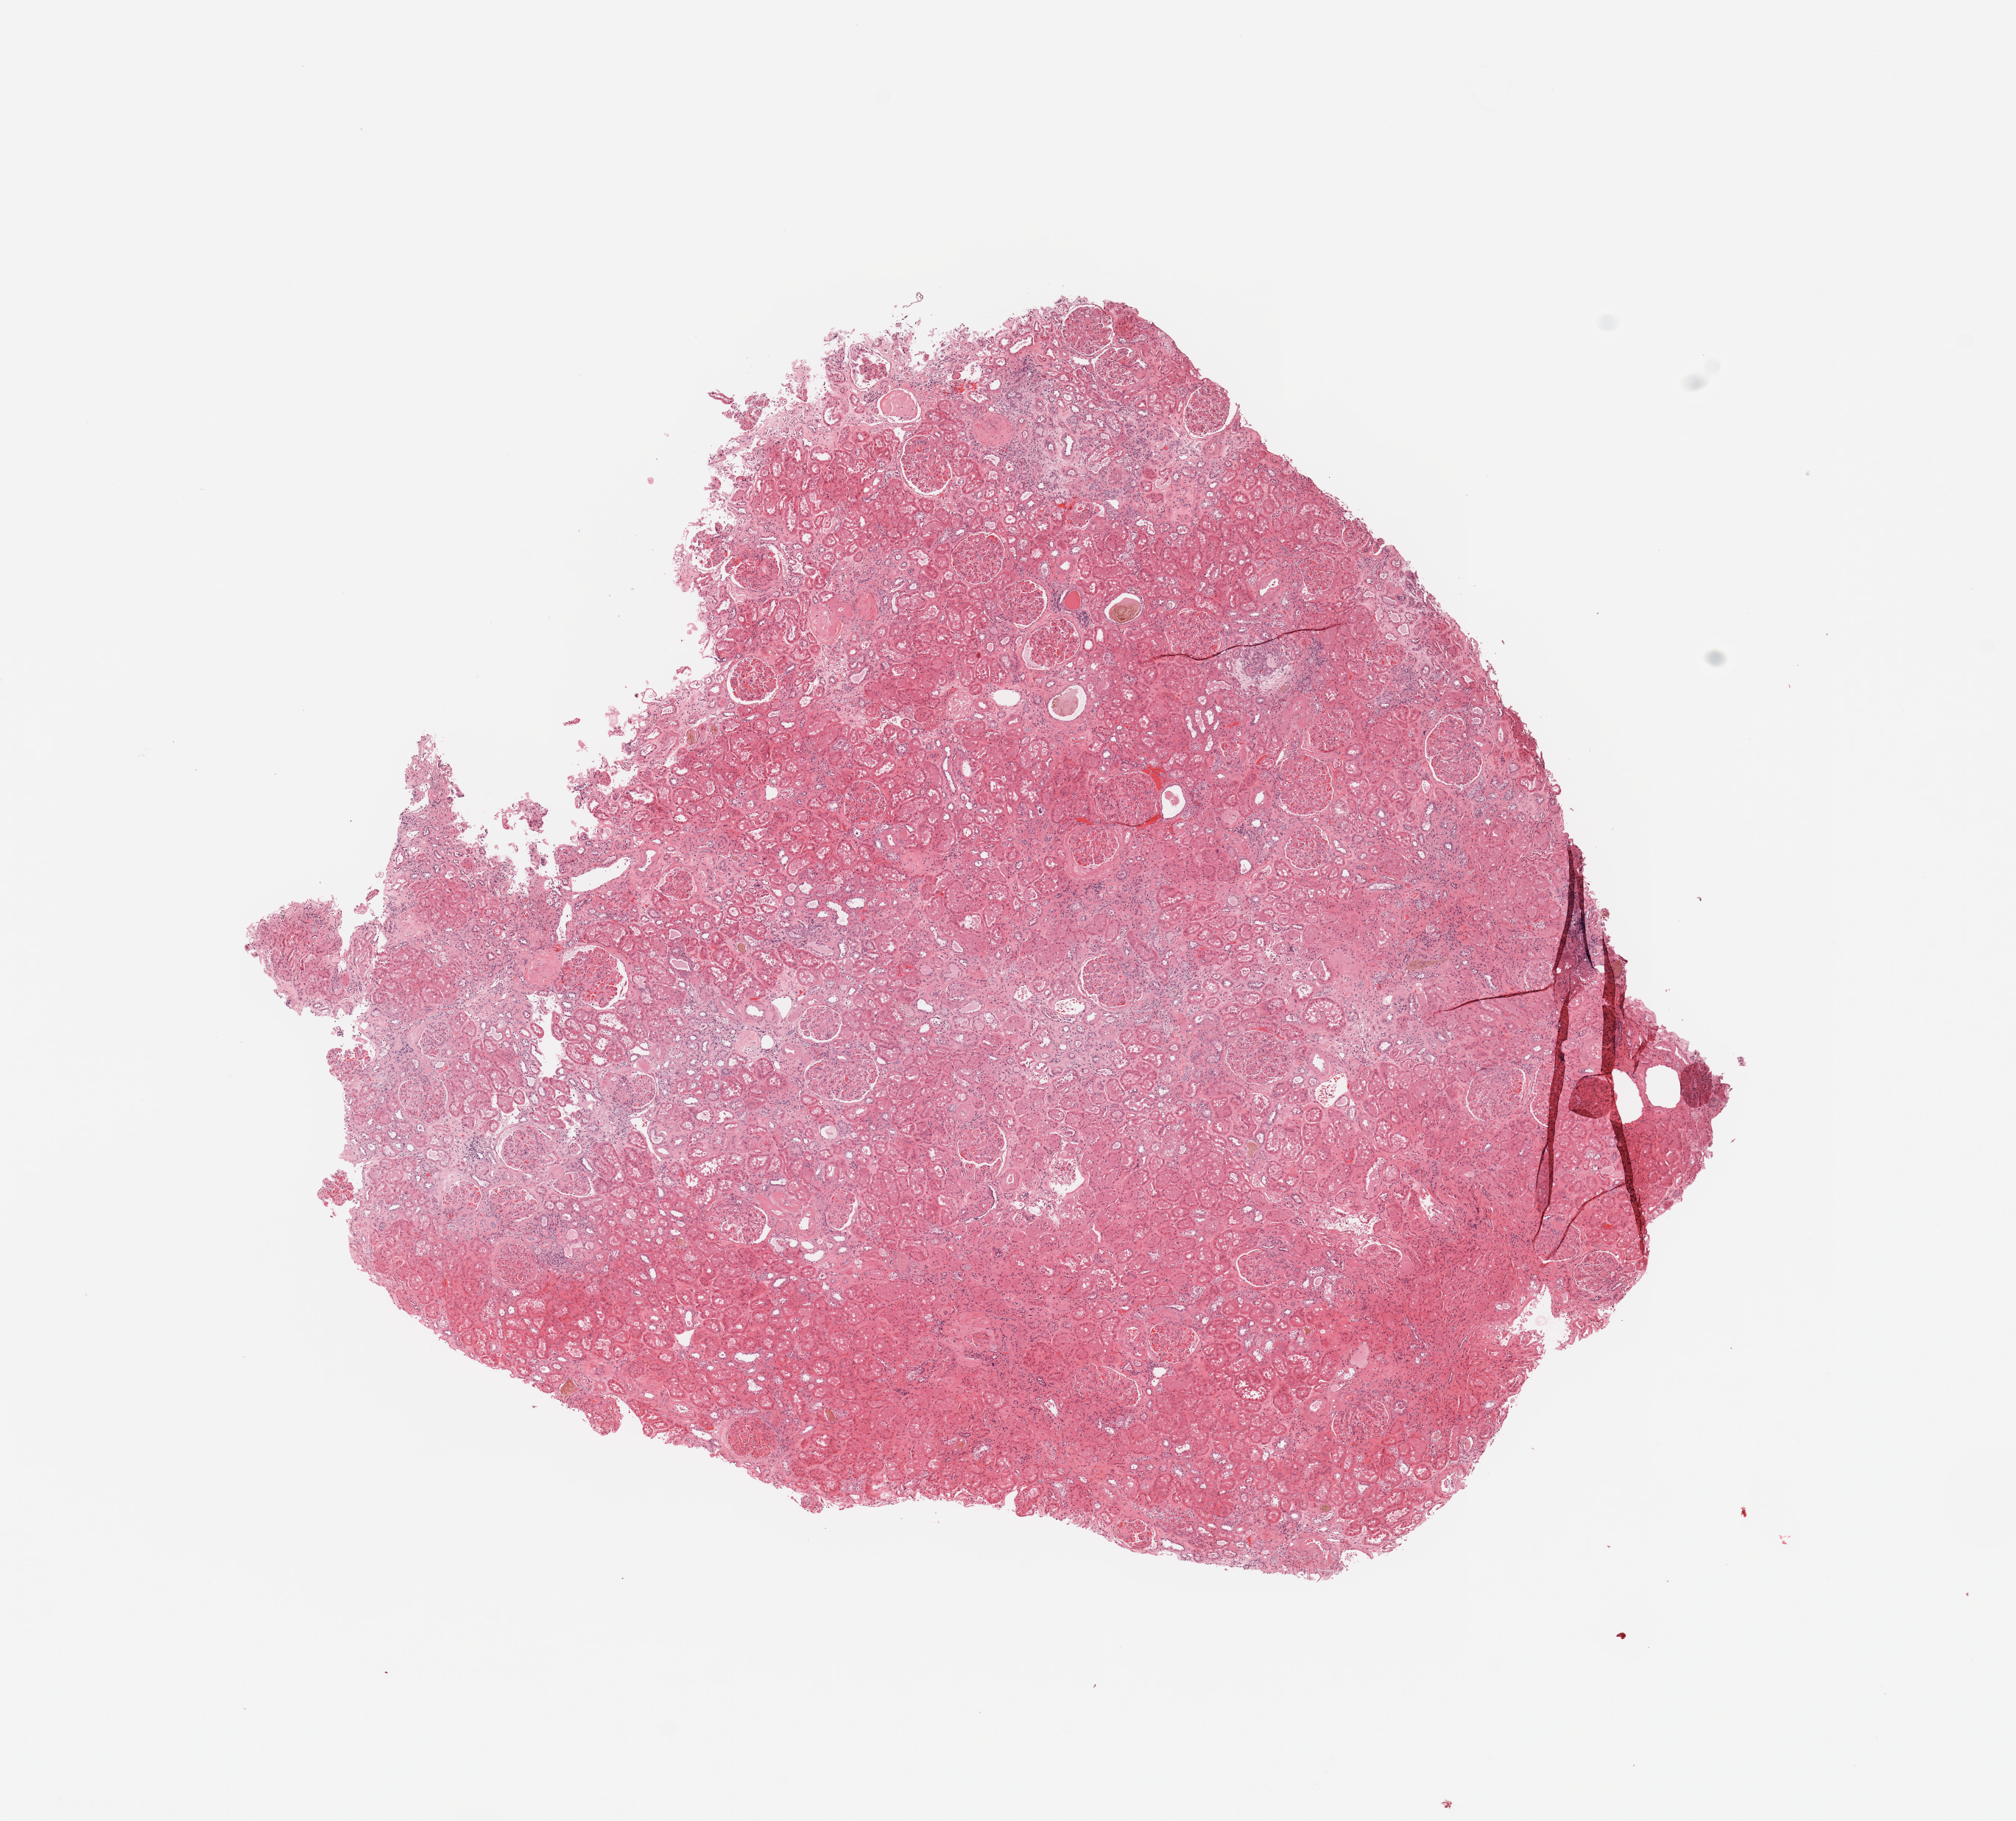
H&E whole-slide image, shown as a low-resolution overview of the whole scanned area (about 10.8 x 9.8 mm, slide scanned at 20x). Normal (non-tumour) tissue sample, sampled site: kidney. Patient: male, age 66 years.
- this section: normal (non-tumour) tissue from the same patient
- patient diagnosis: Renal cell carcinoma, NOS